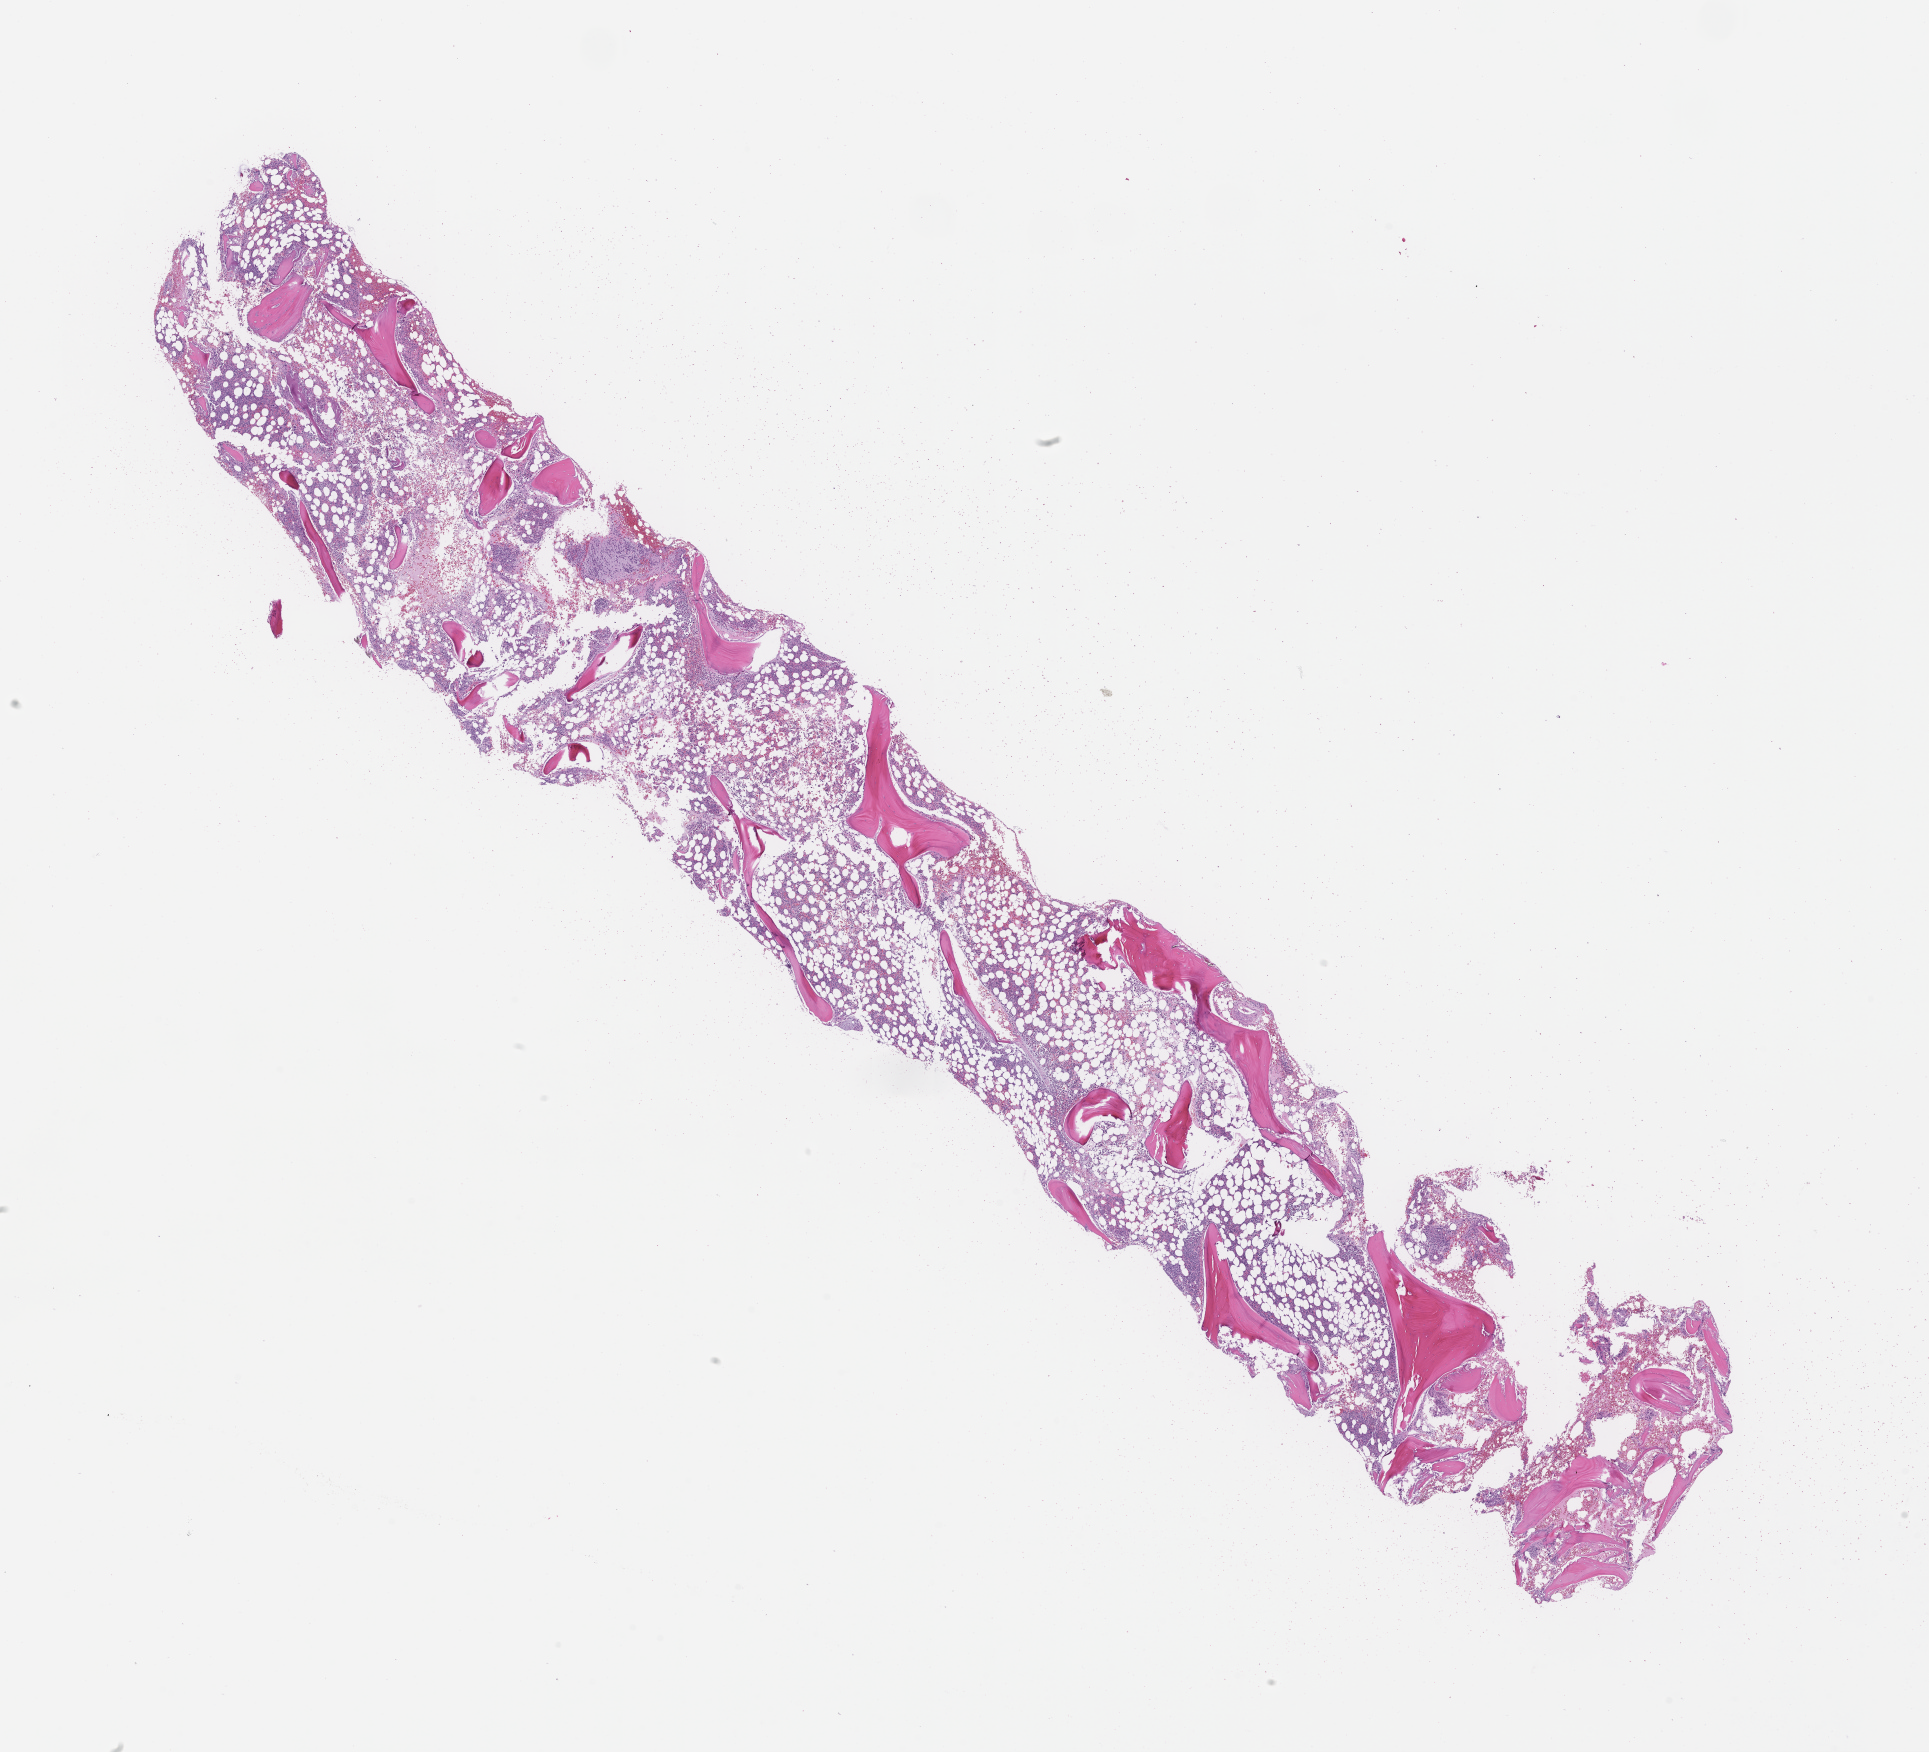
Digitized haematoxylin and eosin-stained section — whole scanned area (about 15.6 x 14.2 mm) shown as a low-resolution overview, FFPE section, tissue site: bone marrow, specimen time point: archival tissue. Patient sex: female.
This section: primary tumour tissue. Diagnosis: Plasma Cell Myeloma.